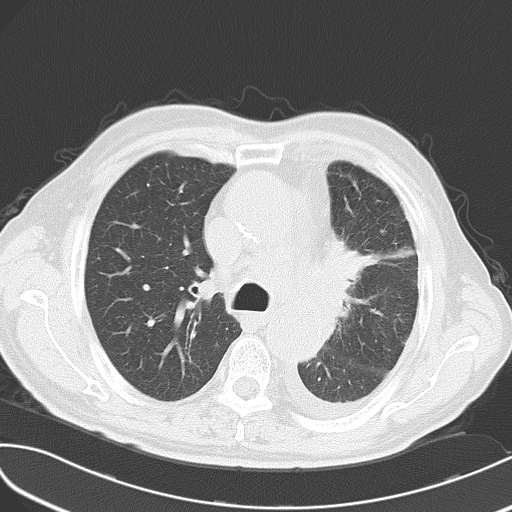
Chest CT, one axial slice. Position 37 of 54 along the scan axis. Lung window (W 1500 / L -600 HU). 5 mm slice thickness. 512 × 512 image matrix, field of view 353 × 353 mm. Male patient, age 70 years. Case-level facts recorded for this patient, not image findings: clinical TNM (as recorded): T2 N1 M3.
Structures marked on this image (bounding box drawn by a radiologist):
- lung tumour (recorded histology: small cell carcinoma): bounding box [x1, y1, x2, y2] px = [323, 228, 387, 299]